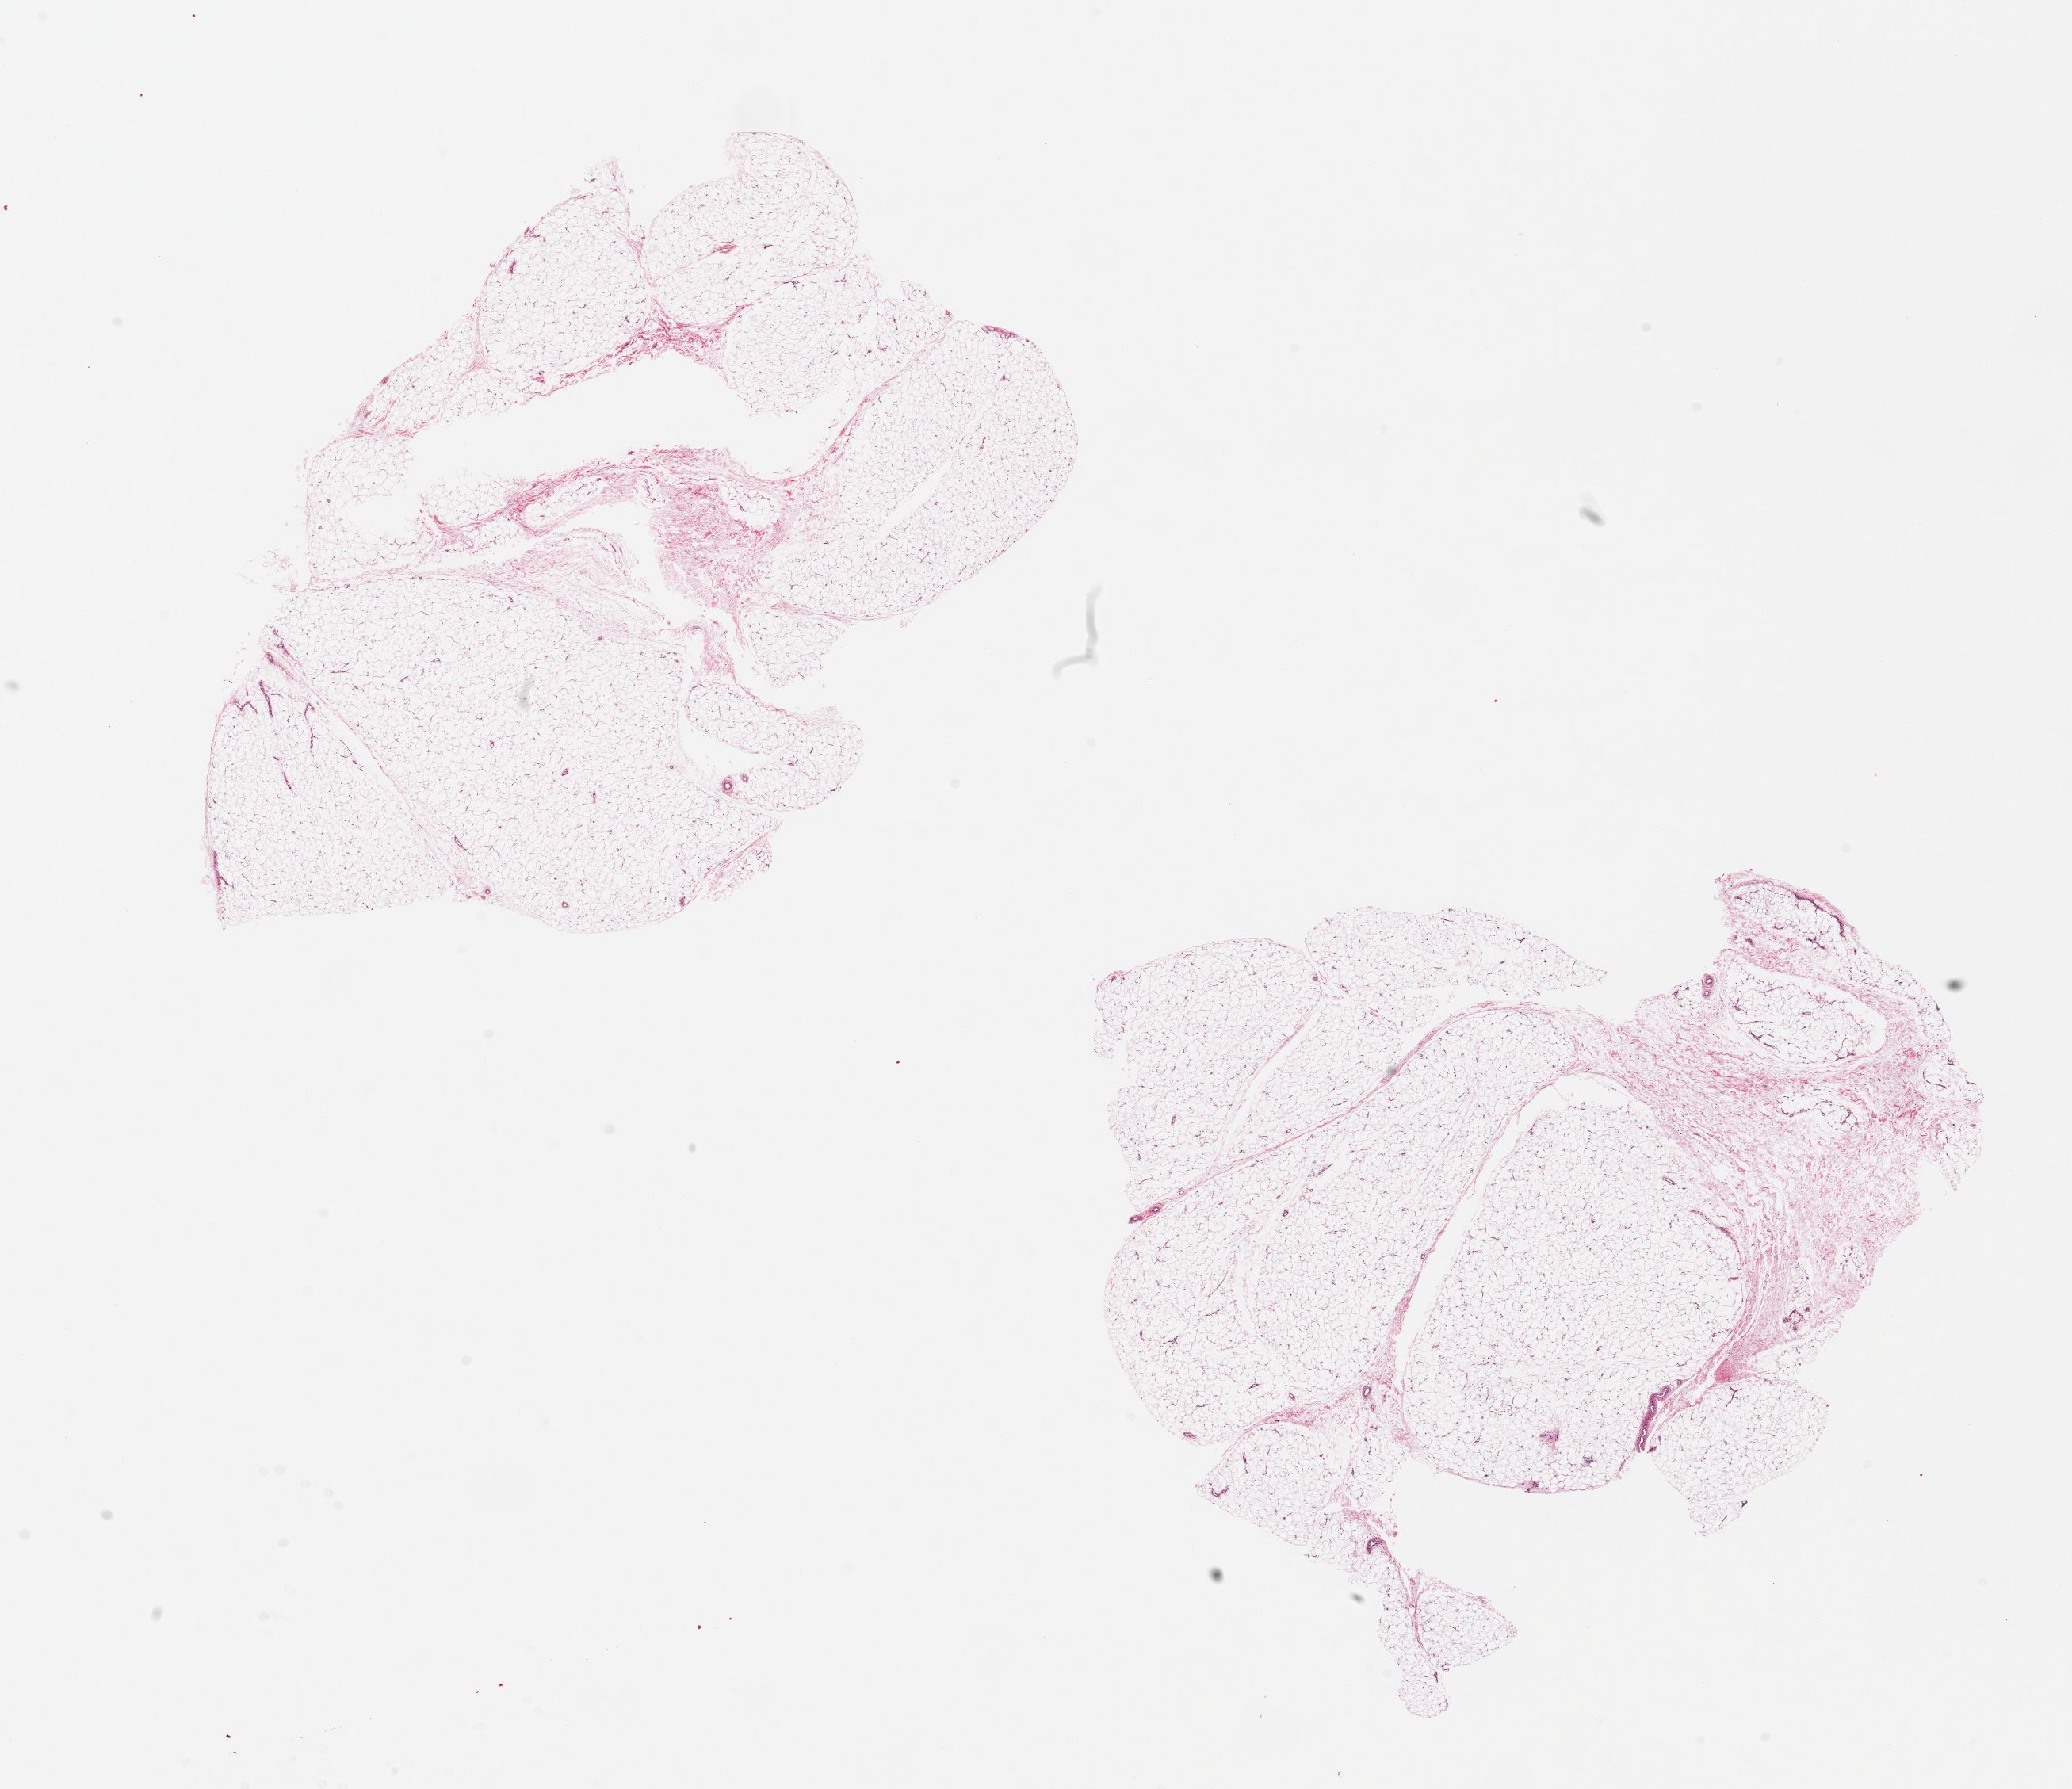
Digitized H&E-stained section, brightfield, whole scanned area (about 20.7 x 17.8 mm, from a 20x scan) shown as a low-resolution overview; PAXgene-fixed, paraffin-embedded tissue; target tissue: adipose tissue; donor tissue sample. Donor sex: female.
* pathologist's review note for this sample: 2 pieces 9x7 & 9x5 mm